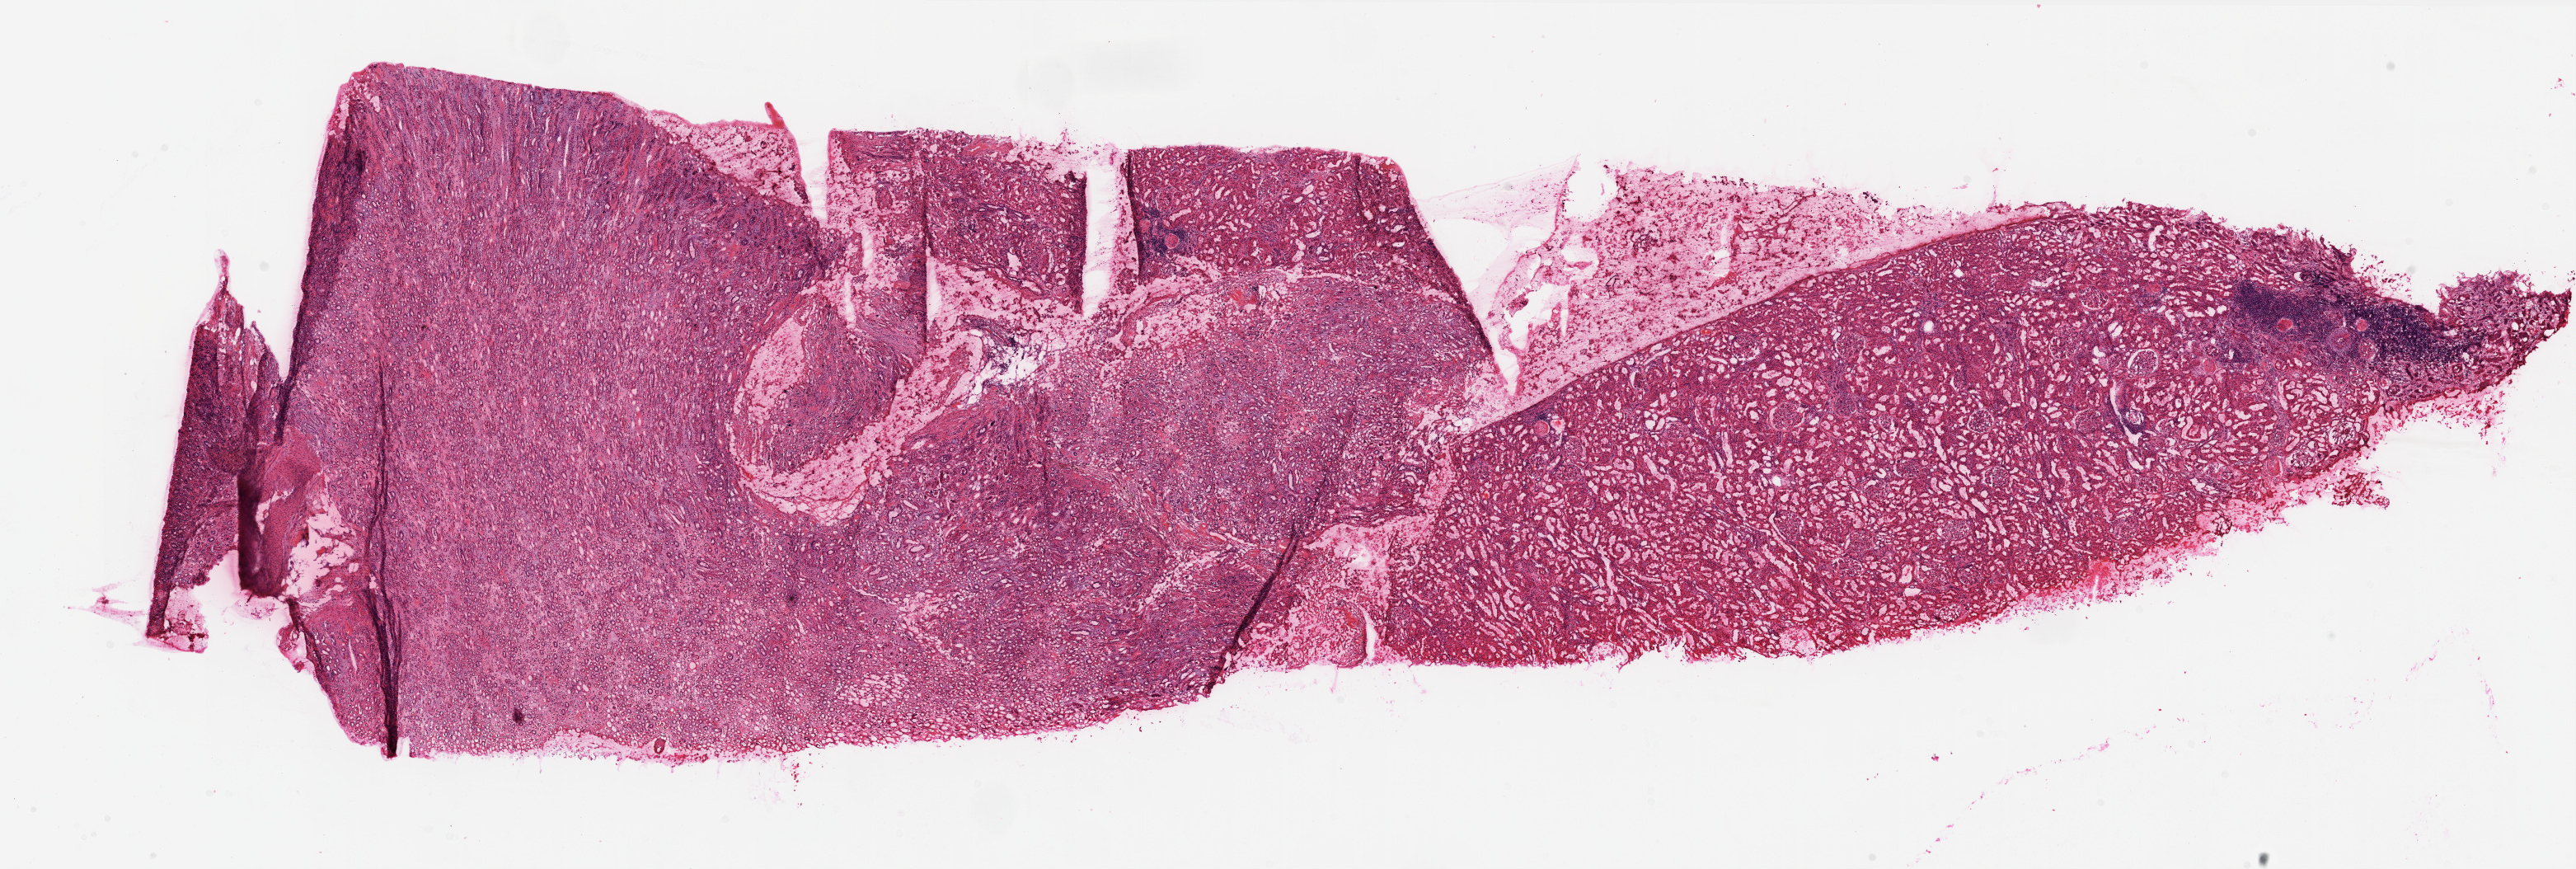
H&E whole-slide image, low-resolution overview of the scanned area, about 25.1 x 8.5 mm (slide scanned at 20x); frozen section from the top of the tissue portion; solid tissue normal (non-tumour tissue) sample from the kidney. Male patient; age at initial diagnosis 63 years.
- this section: solid tissue normal sample (biorepository sample class)
- patient diagnosis: Clear cell adenocarcinoma, NOS